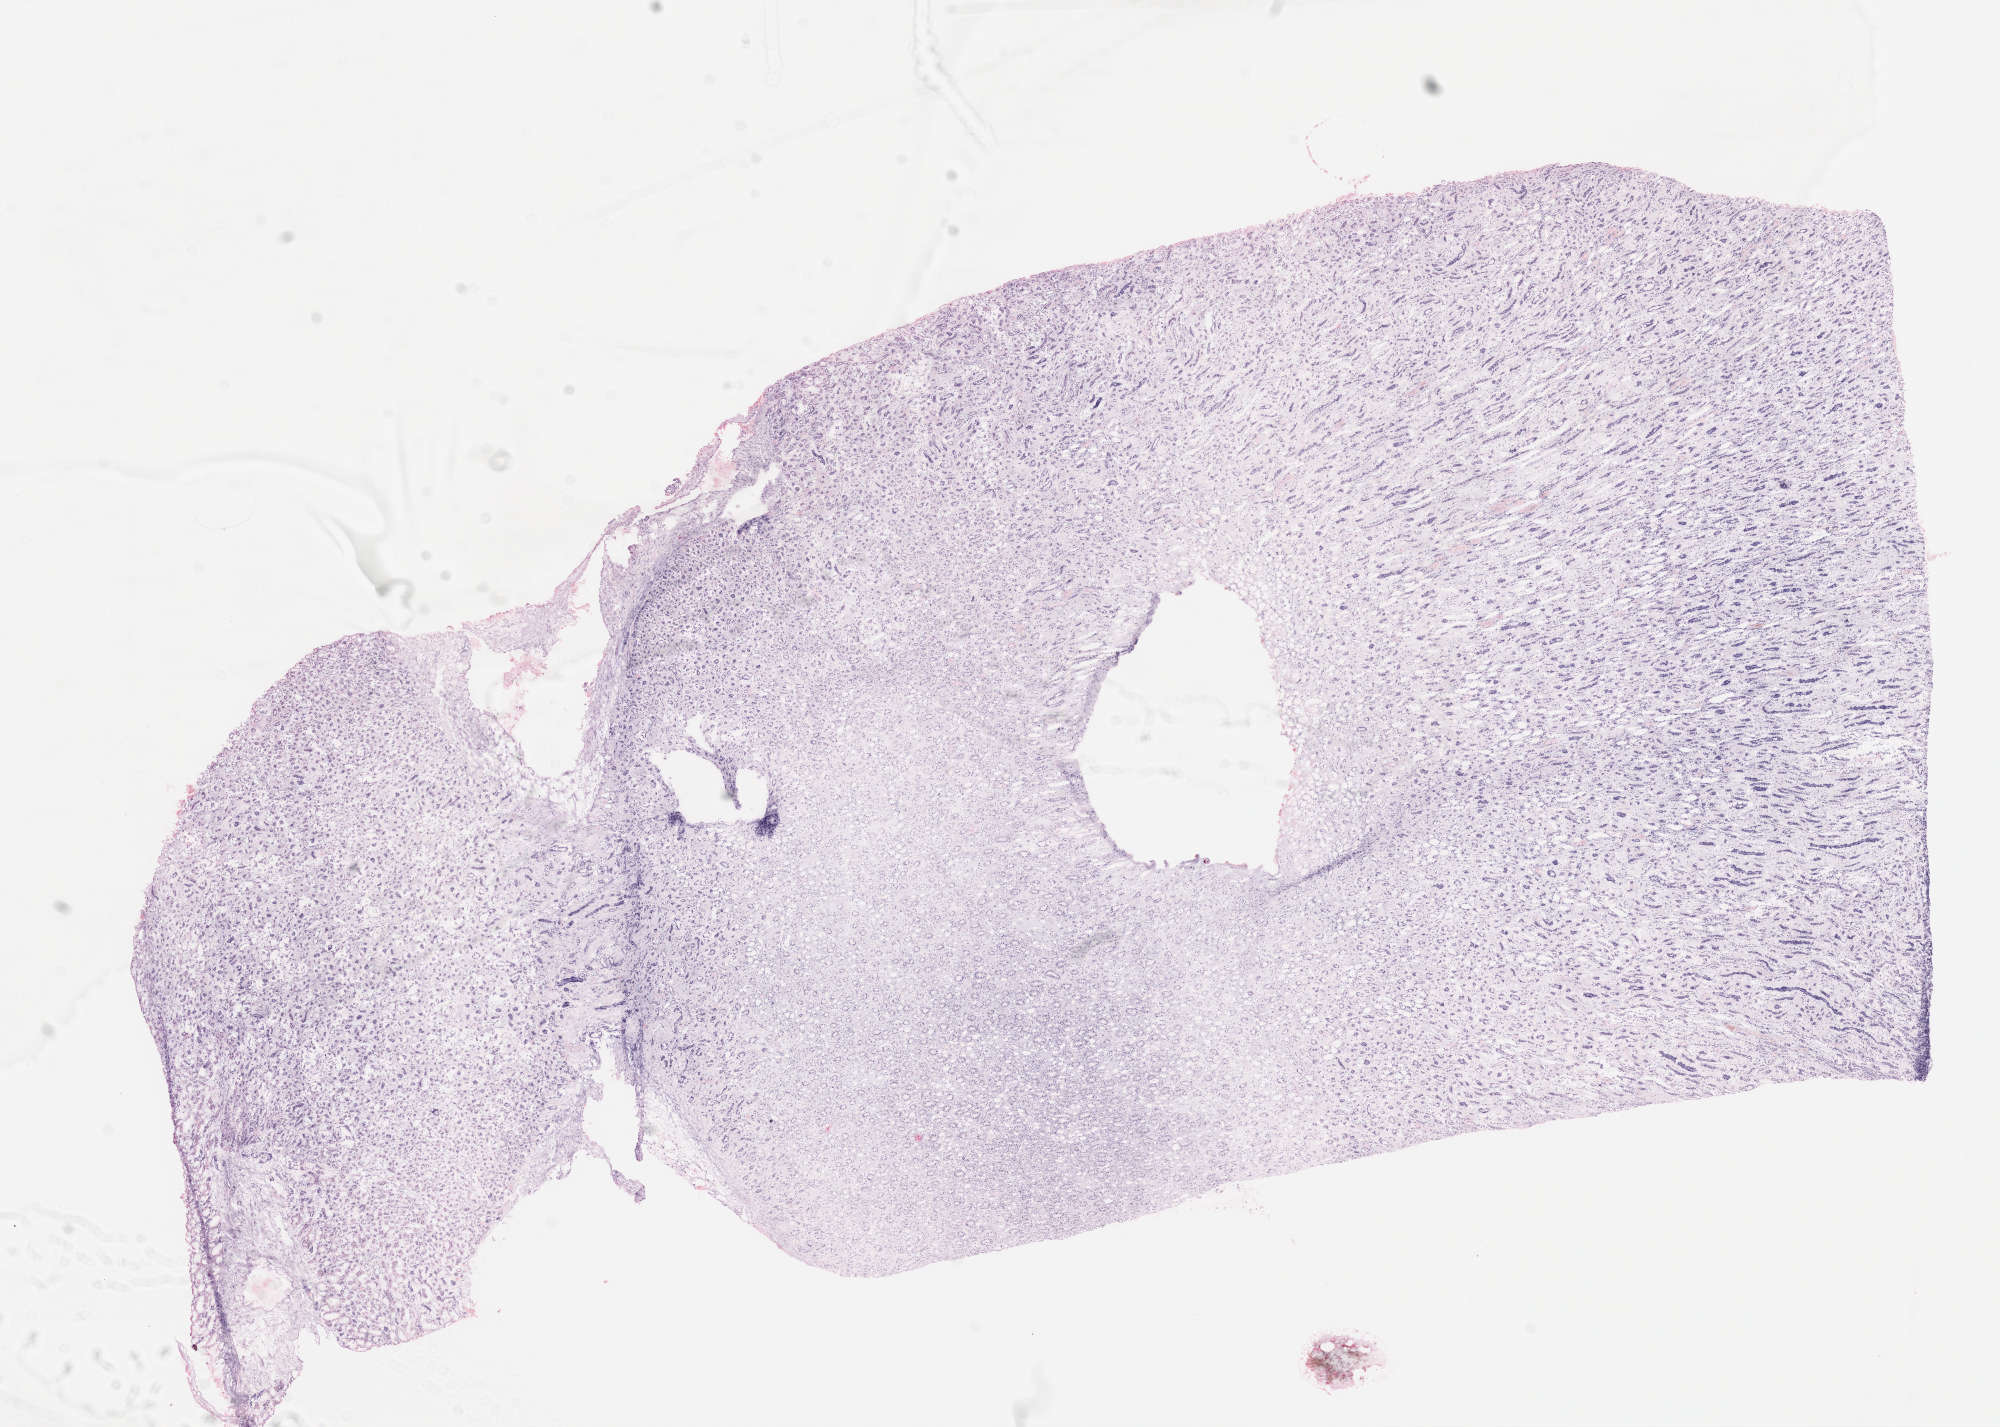
Digitized H&E tissue section (whole slide) — shown as a low-resolution overview of the whole scanned area (about 16.0 x 11.5 mm), frozen section from the top of the tissue portion, sample: solid tissue normal (non-tumour tissue), kidney. Male patient; age at initial diagnosis 69 years.
This section: solid tissue normal (non-tumour) sample from the same patient. Patient diagnosis: Clear cell adenocarcinoma, NOS.